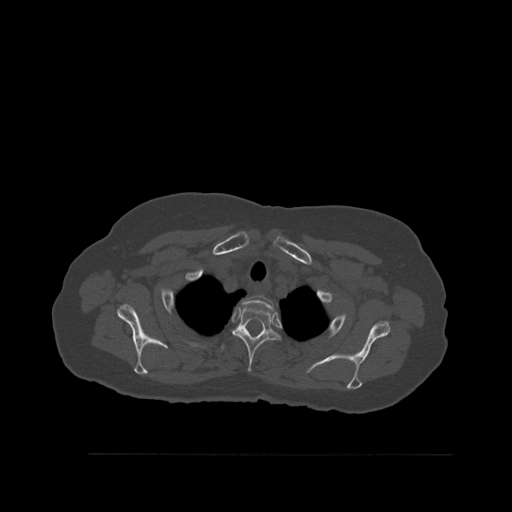
CT including the spine, one axial slice; position 432 of 527 along the scan axis; bone window (W 1800 / L 400 HU); 512 × 512 image matrix. Patient: female, 73 years. Case-level facts recorded for this patient, not image findings: primary cancer: breast; vertebrae with lytic lesions (as recorded): L2.
Structures marked on this image (semi-automatic segmentation, software-assisted and operator-edited):
- T1 vertebra: bounding box [x1, y1, x2, y2] px = [243, 296, 274, 310]
- T2 vertebra: [232, 306, 280, 373]
- T3 vertebra: [221, 343, 227, 351]